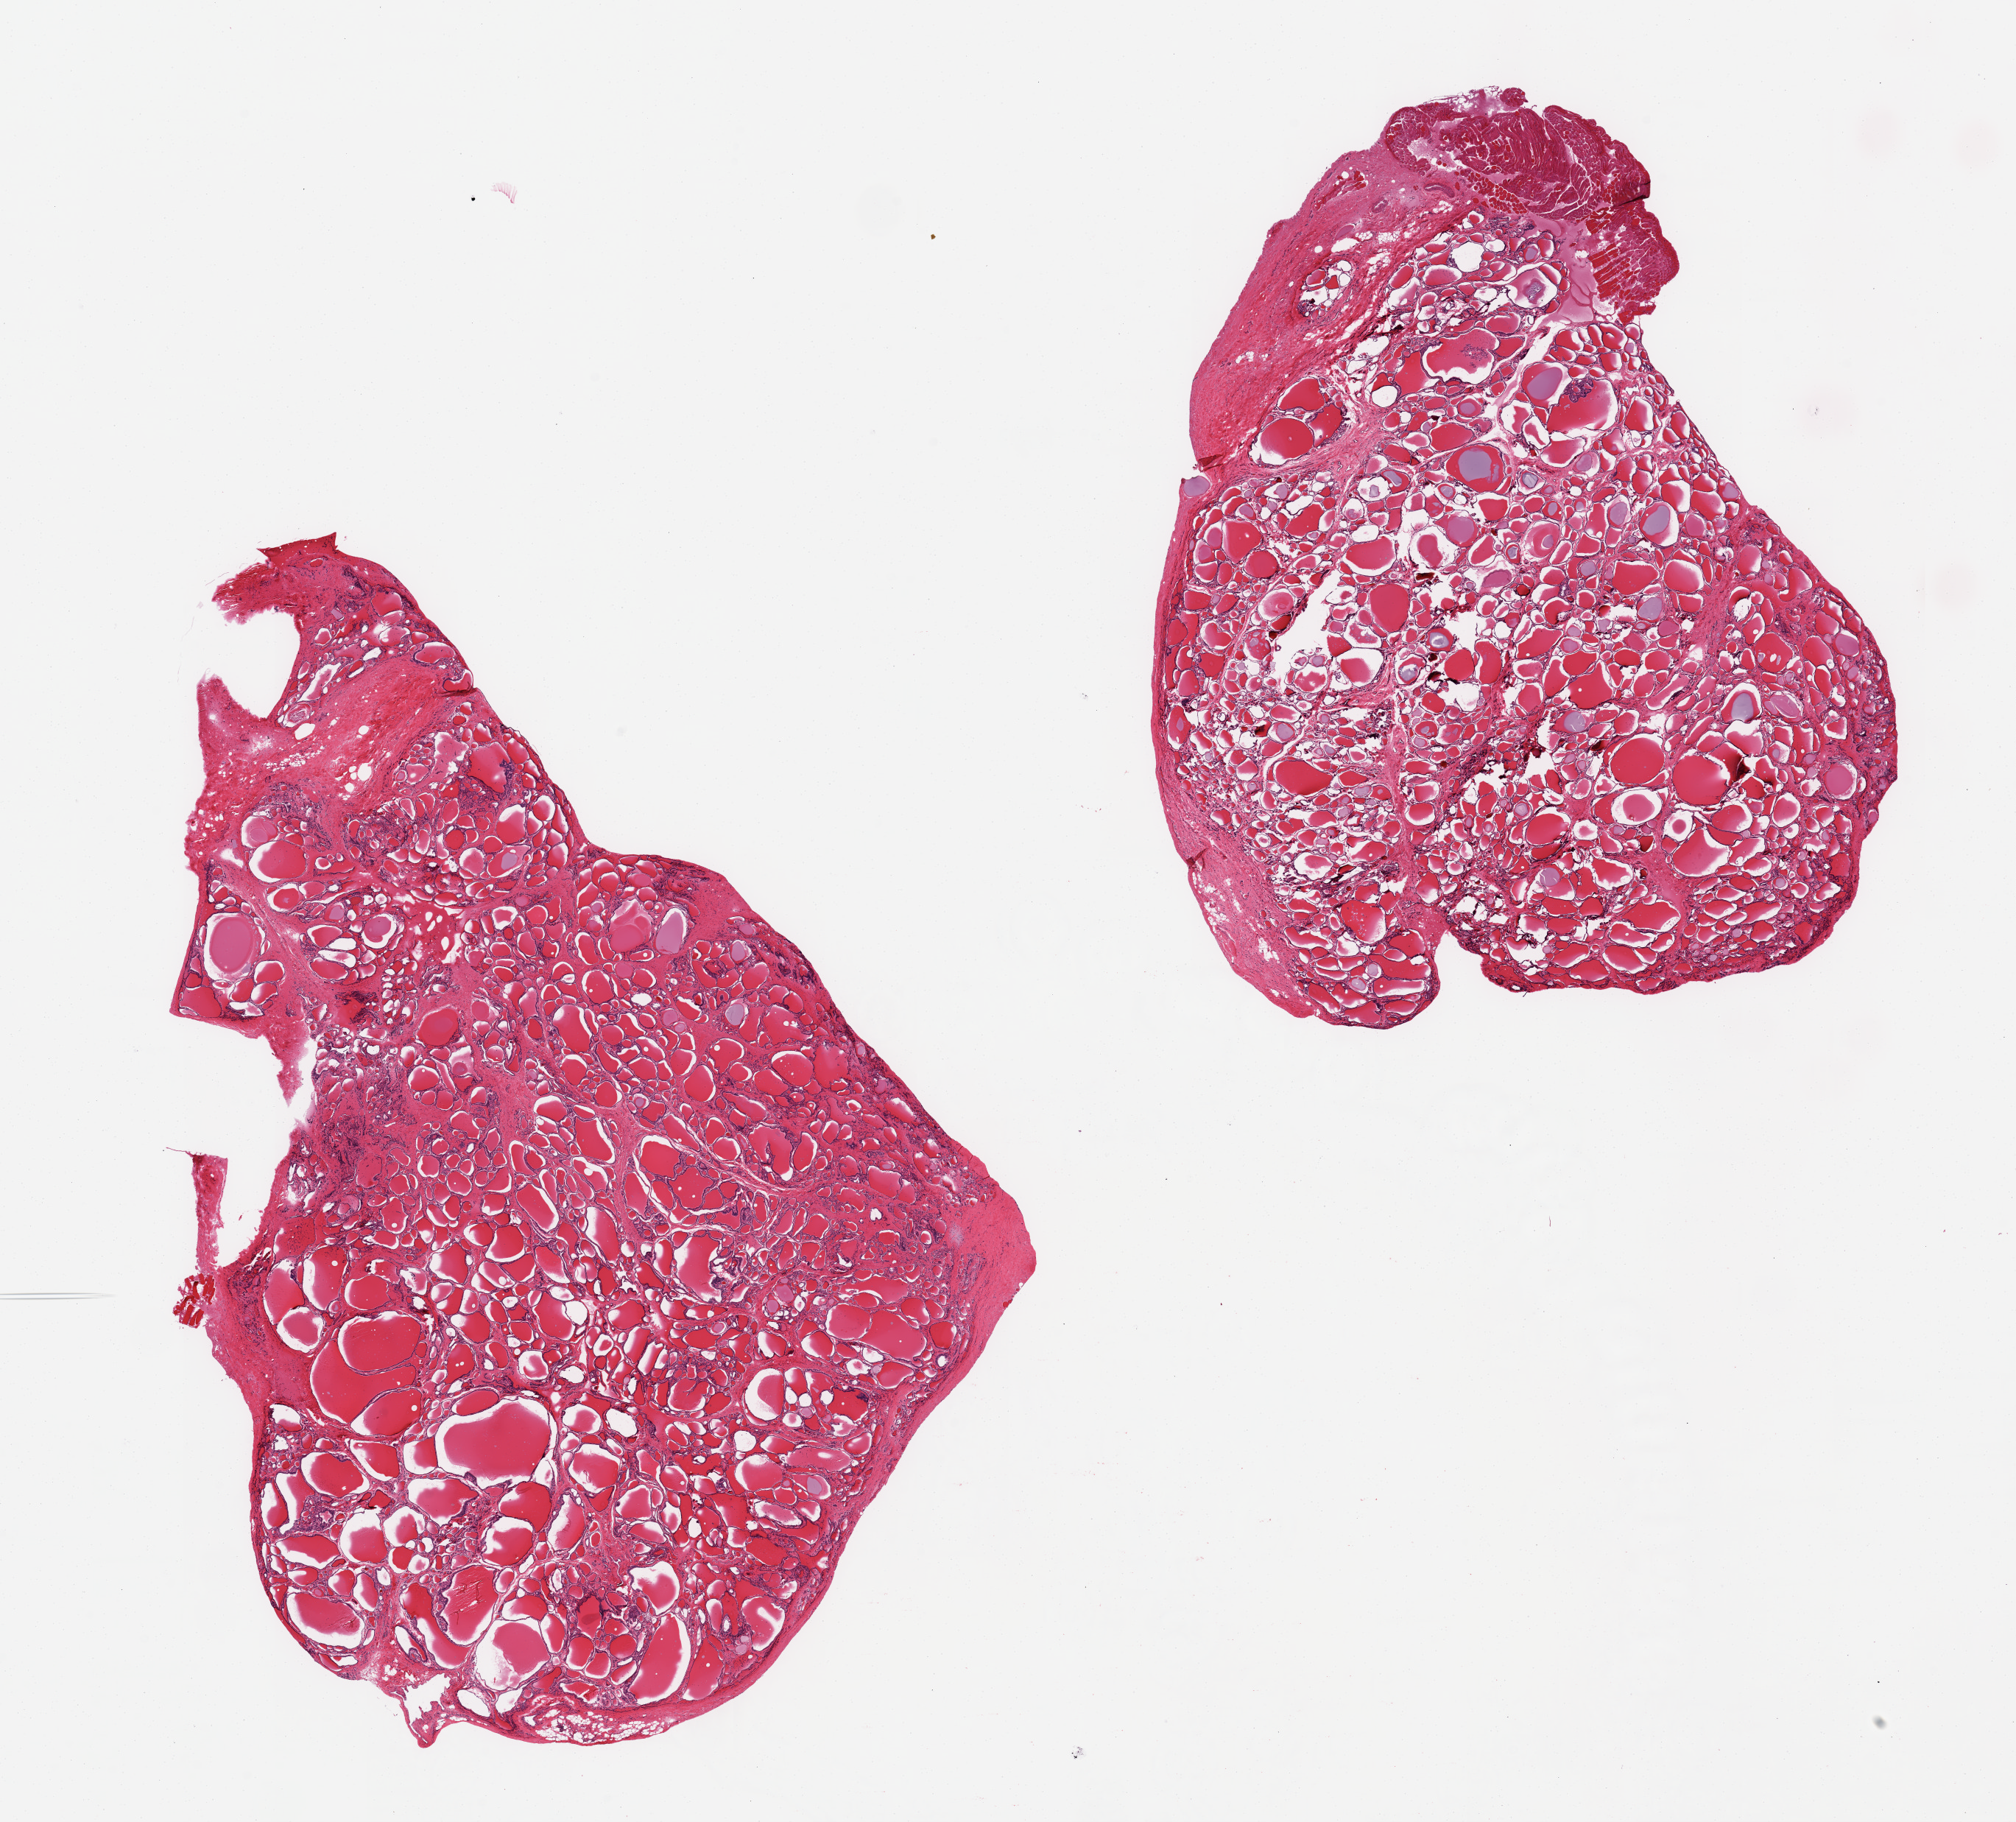
Hematoxylin and eosin (H&E) whole-slide image, a low-resolution overview of the entire scanned area, about 21.7 x 19.6 mm (slide scanned at 20x). PAXgene-fixed paraffin-embedded (PFPE) section. Section of thyroid (target tissue). Tissue donor sample. Female donor.
- pathologist's review note for this sample: 2 pieces, no abnormality